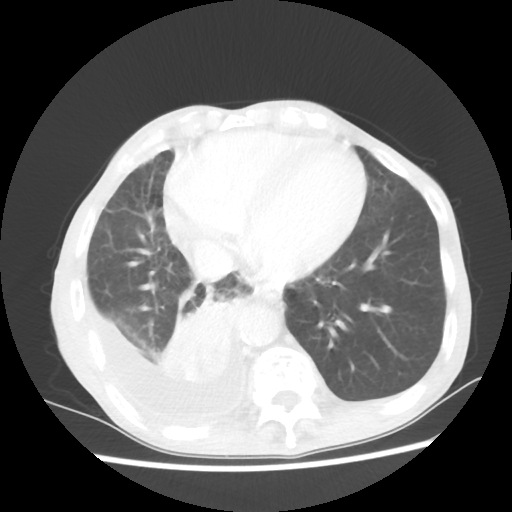
Chest CT, one axial slice. Slice 19 of 60 in the series (ordered by position). 80 kVp. Lung window (W 1500 / L -600 HU). 5 mm slice thickness. 512 × 512 image matrix, field of view 335 × 335 mm. Male patient, age 76 years. From the clinical record (not read from this slice): clinical TNM (as recorded): T3 N3 M1a; histopathological grade: G3.
Outlined on this slice (rectangle marked by the reading radiologist):
- lung tumour (recorded histology: squamous cell carcinoma): bounding box [x1, y1, x2, y2] px = [156, 286, 243, 387]